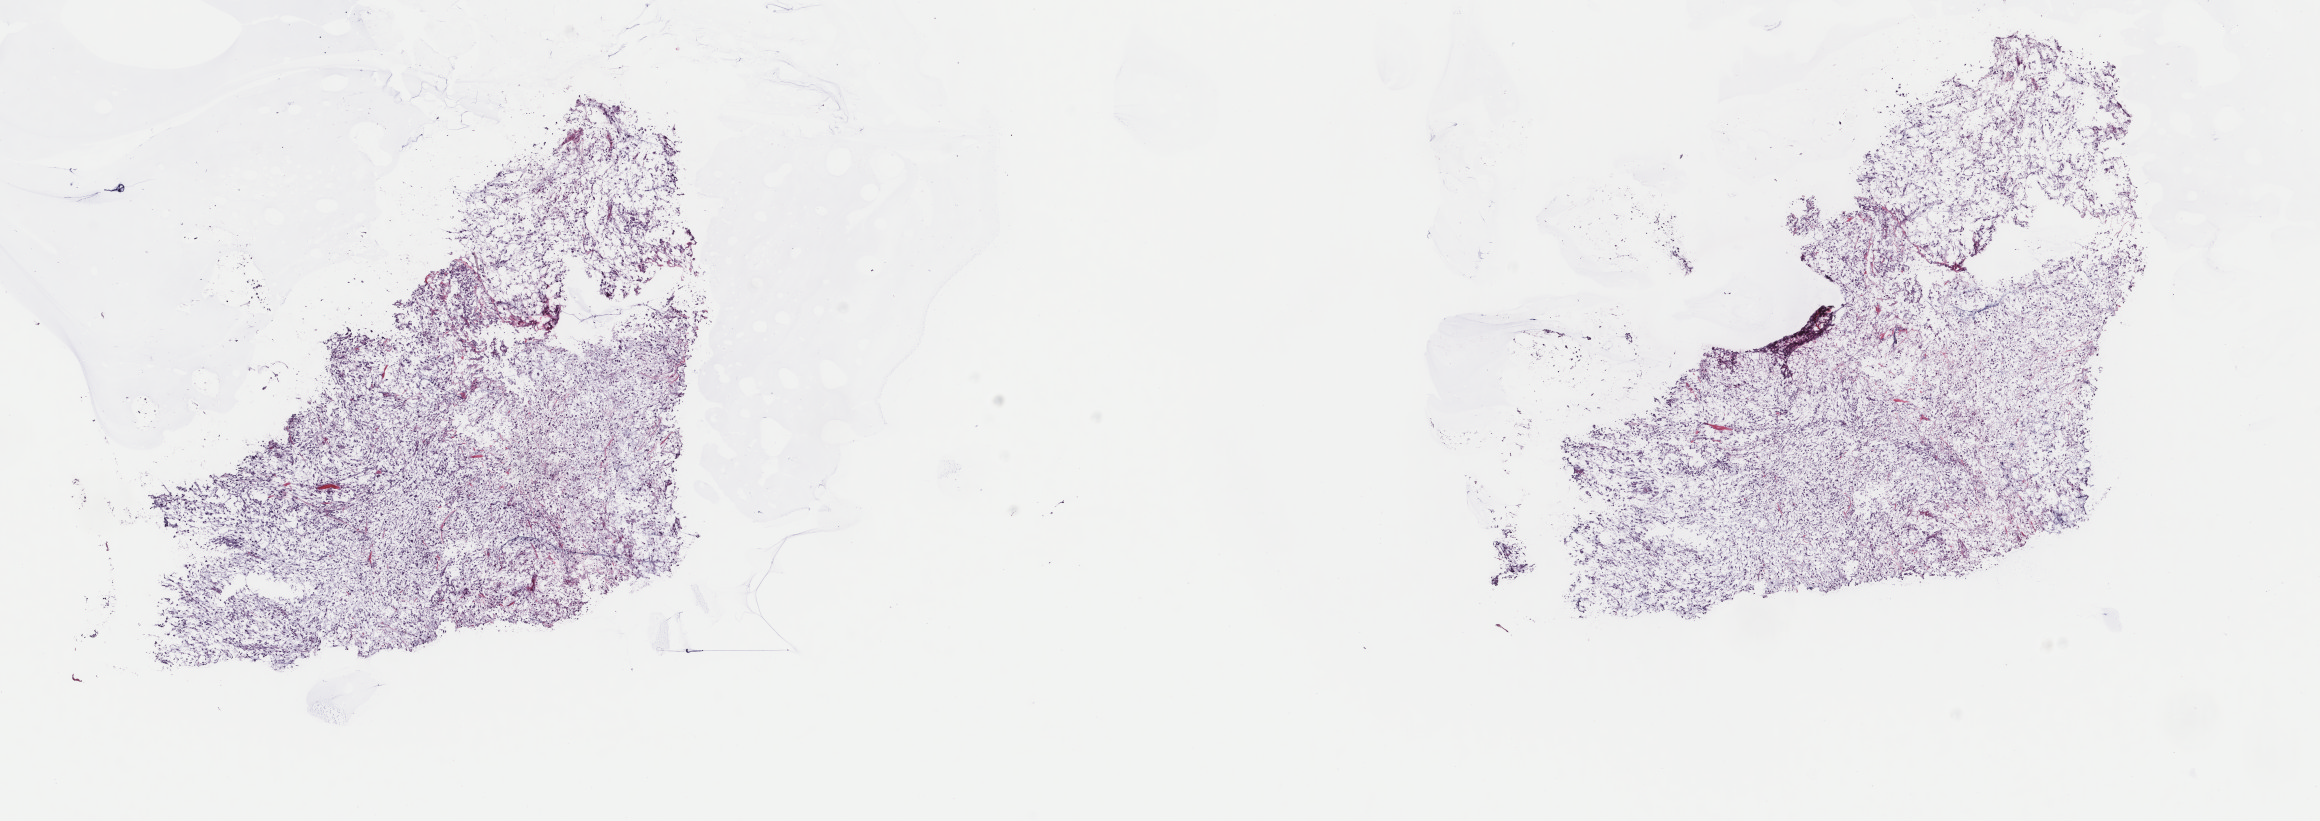
Hematoxylin and eosin (H&E) stained whole-slide image — low-resolution overview of the scanned area, about 18.4 x 6.5 mm (acquisition: 40x scan), frozen section from the top of the tissue portion, metastatic tumour sample. Female patient; age at initial diagnosis 58 years.
This section: metastatic tumour tissue. Patient diagnosis: Malignant melanoma, NOS.